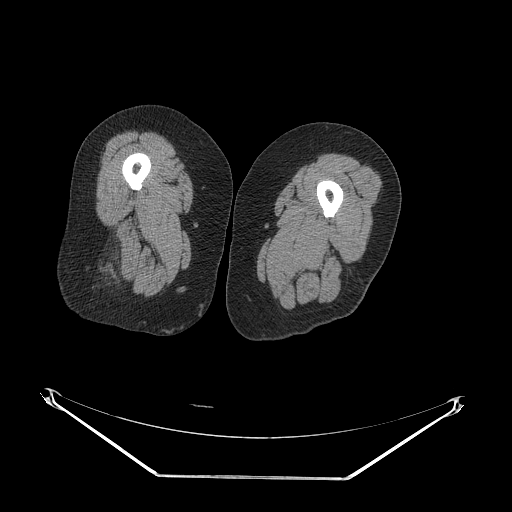
CT of an extremity soft-tissue mass (from a PET/CT study), one axial slice. Position 23 of 257 along the scan axis. Reconstruction kernel STANDARD. 140 kVp. Soft-tissue window (W 400 / L 40 HU). 3.75 mm slice thickness. 512 × 512 image matrix, field of view 500 × 500 mm. Female patient. Case-level facts recorded for this patient, not image findings: histological type: synovial sarcoma; grade: intermediate; site of the primary tumour: right buttock.
Annotated regions visible in this slice (expert contour drawn on MRI and transferred to this co-registered scan by the dataset authors):
- gross tumour volume including surrounding oedema: bounding box <94,238,115,280> (left, top, right, bottom; pixels)